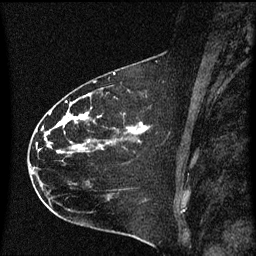
Breast MRI (dynamic contrast-enhanced), one sagittal slice. Position 38 of 60 along the scan axis. Dynamic contrast-enhanced series, image 2 of 3 at this slice position (ordered by acquisition). 1.5 T. TE 4.2 ms, TR 8.4 ms. 256 × 256 image matrix. Female patient, age 35 years. From the clinical record (not read from this slice): setting: breast cancer imaged before/during neoadjuvant chemotherapy; receptor status: HER2-positive.
Structures marked on this image (semi-automatically segmented with operator editing):
- analysis volume of interest (the breast-tissue region the enhancement analysis was run in; not a lesion): box from (x=30, y=68) to (x=174, y=173) px
- tumour enhancement mask (voxels above the 70 % enhancement threshold inside the analysis volume of interest): (x=47, y=94)–(x=148, y=151)